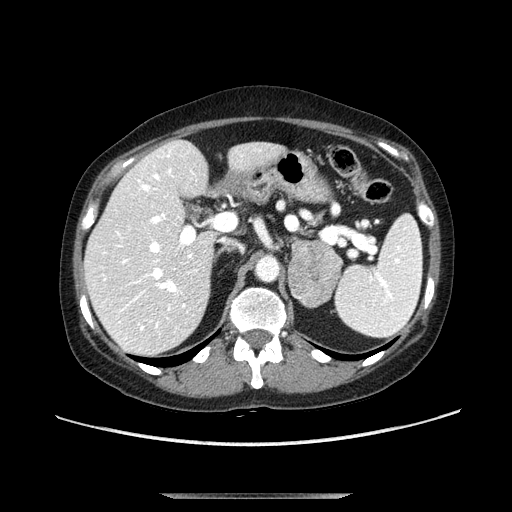
Contrast-enhanced abdominal CT, one axial slice. Slice 68 of 107 in the series (ordered by position). Soft-tissue window (W 400 / L 40 HU). 2.5 mm slice thickness. 512 × 512 image matrix. Female patient. From the clinical record (not read from this slice): diagnosis: adrenocortical carcinoma; tumour side: left adrenal; tumour size at pathology: 7.5 cm; Ki-67 index: 9 %.
Outlined on this slice (semi-automatic segmentation, software-assisted and operator-edited):
- mass: bounding box (x1, y1, x2, y2) in pixels: (288, 240, 343, 307)